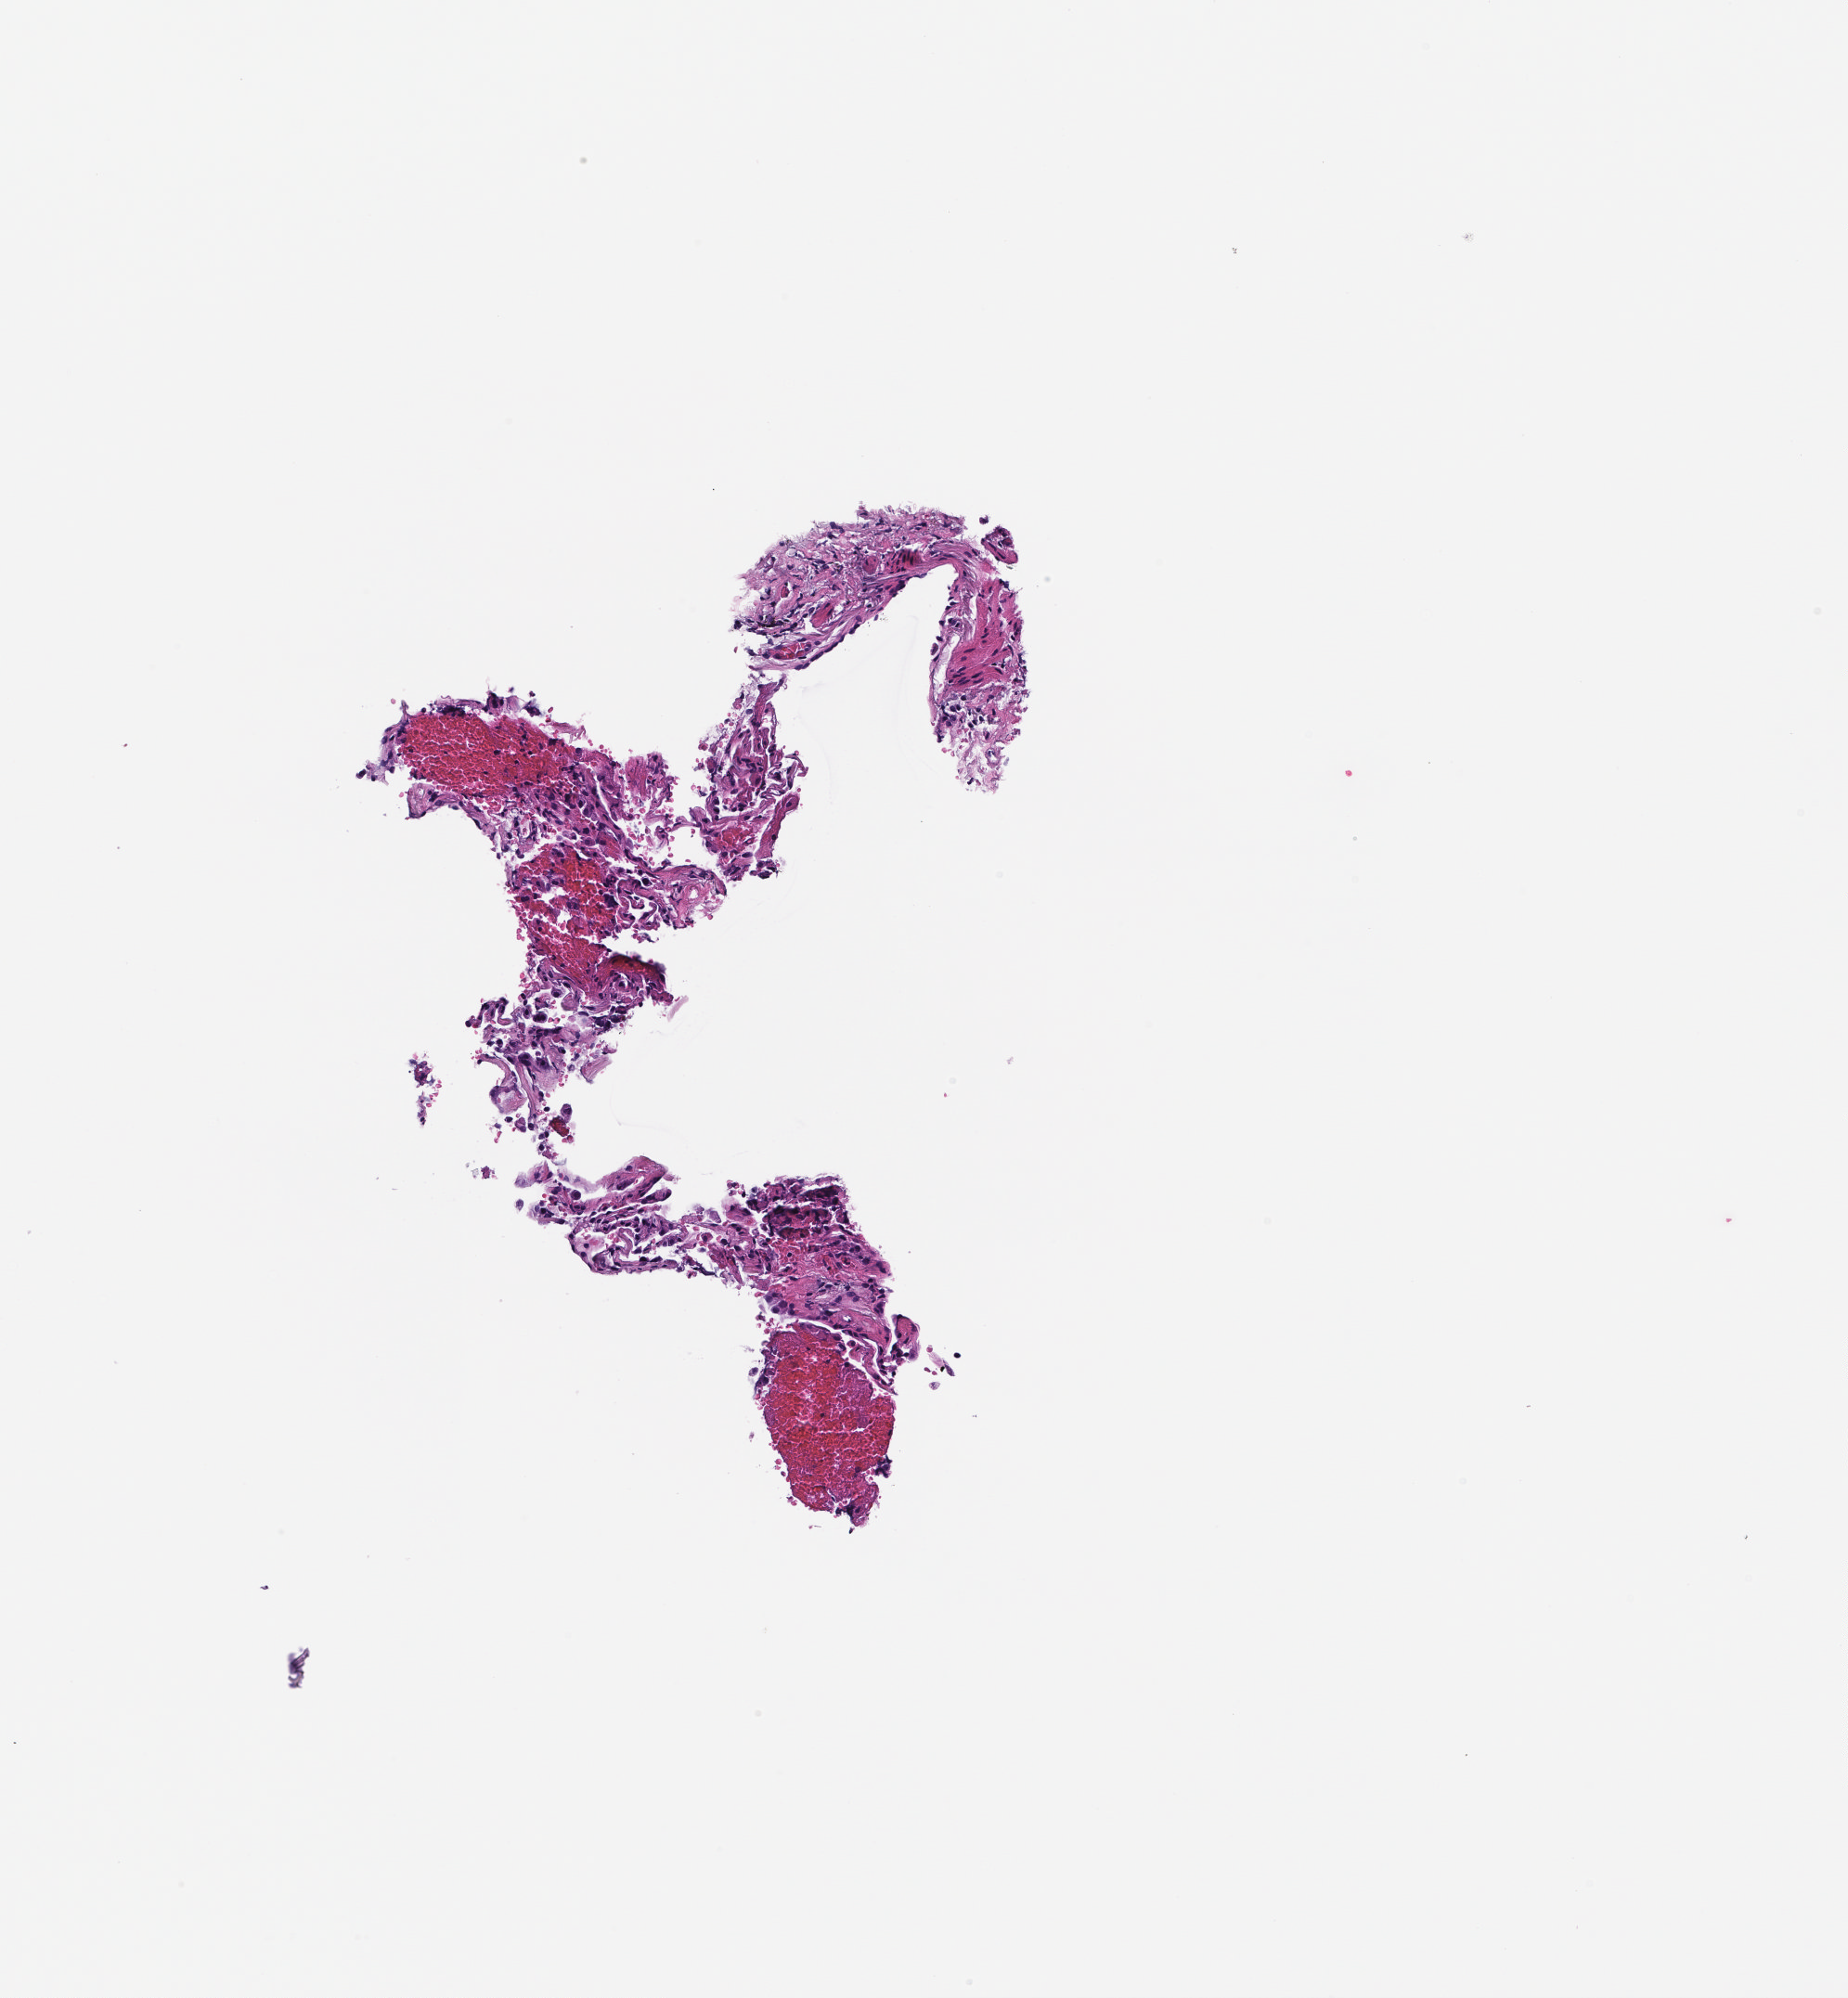
Whole-slide image, hematoxylin and eosin (H&E) stain — a low-resolution overview of the entire scanned area, about 2.0 x 2.2 mm, FFPE section. Patient sex: male.
This section: metastasis (sampled organ not recorded). Primary diagnosis of the patient: Colorectal Carcinoma.